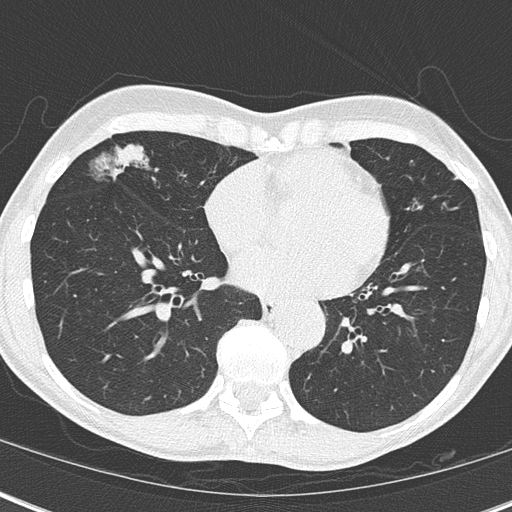
Chest CT (low-dose screening protocol), one axial image; third annual screen; lung window (W 1500 / L -600 HU); lung (sharp) reconstruction kernel (B50f); slice 106 of 173 in the series; 512 × 512 image matrix. Female, age 67 years at enrolment. Current smoker at enrolment.
Lesion marked by an expert reader, bounding box <91,137,187,217> (left, top, right, bottom; pixels). The exam's reader record, not a measurement of the box and not confirmed to be the same lesion: non-calcified nodule or mass ≥4 mm, right middle lobe, 32 × 17 mm, mixed attenuation, pre-existing on the prior screen: yes; interval growth: yes. Official screen result: positive, other. Later outcome: lung cancer diagnosed 76 days after this screen — bronchiolo-alveolar adenocarcinoma, NOS, right middle lobe, well differentiated (G1), stage IA (AJCC 6th edition), 25 mm at pathology.